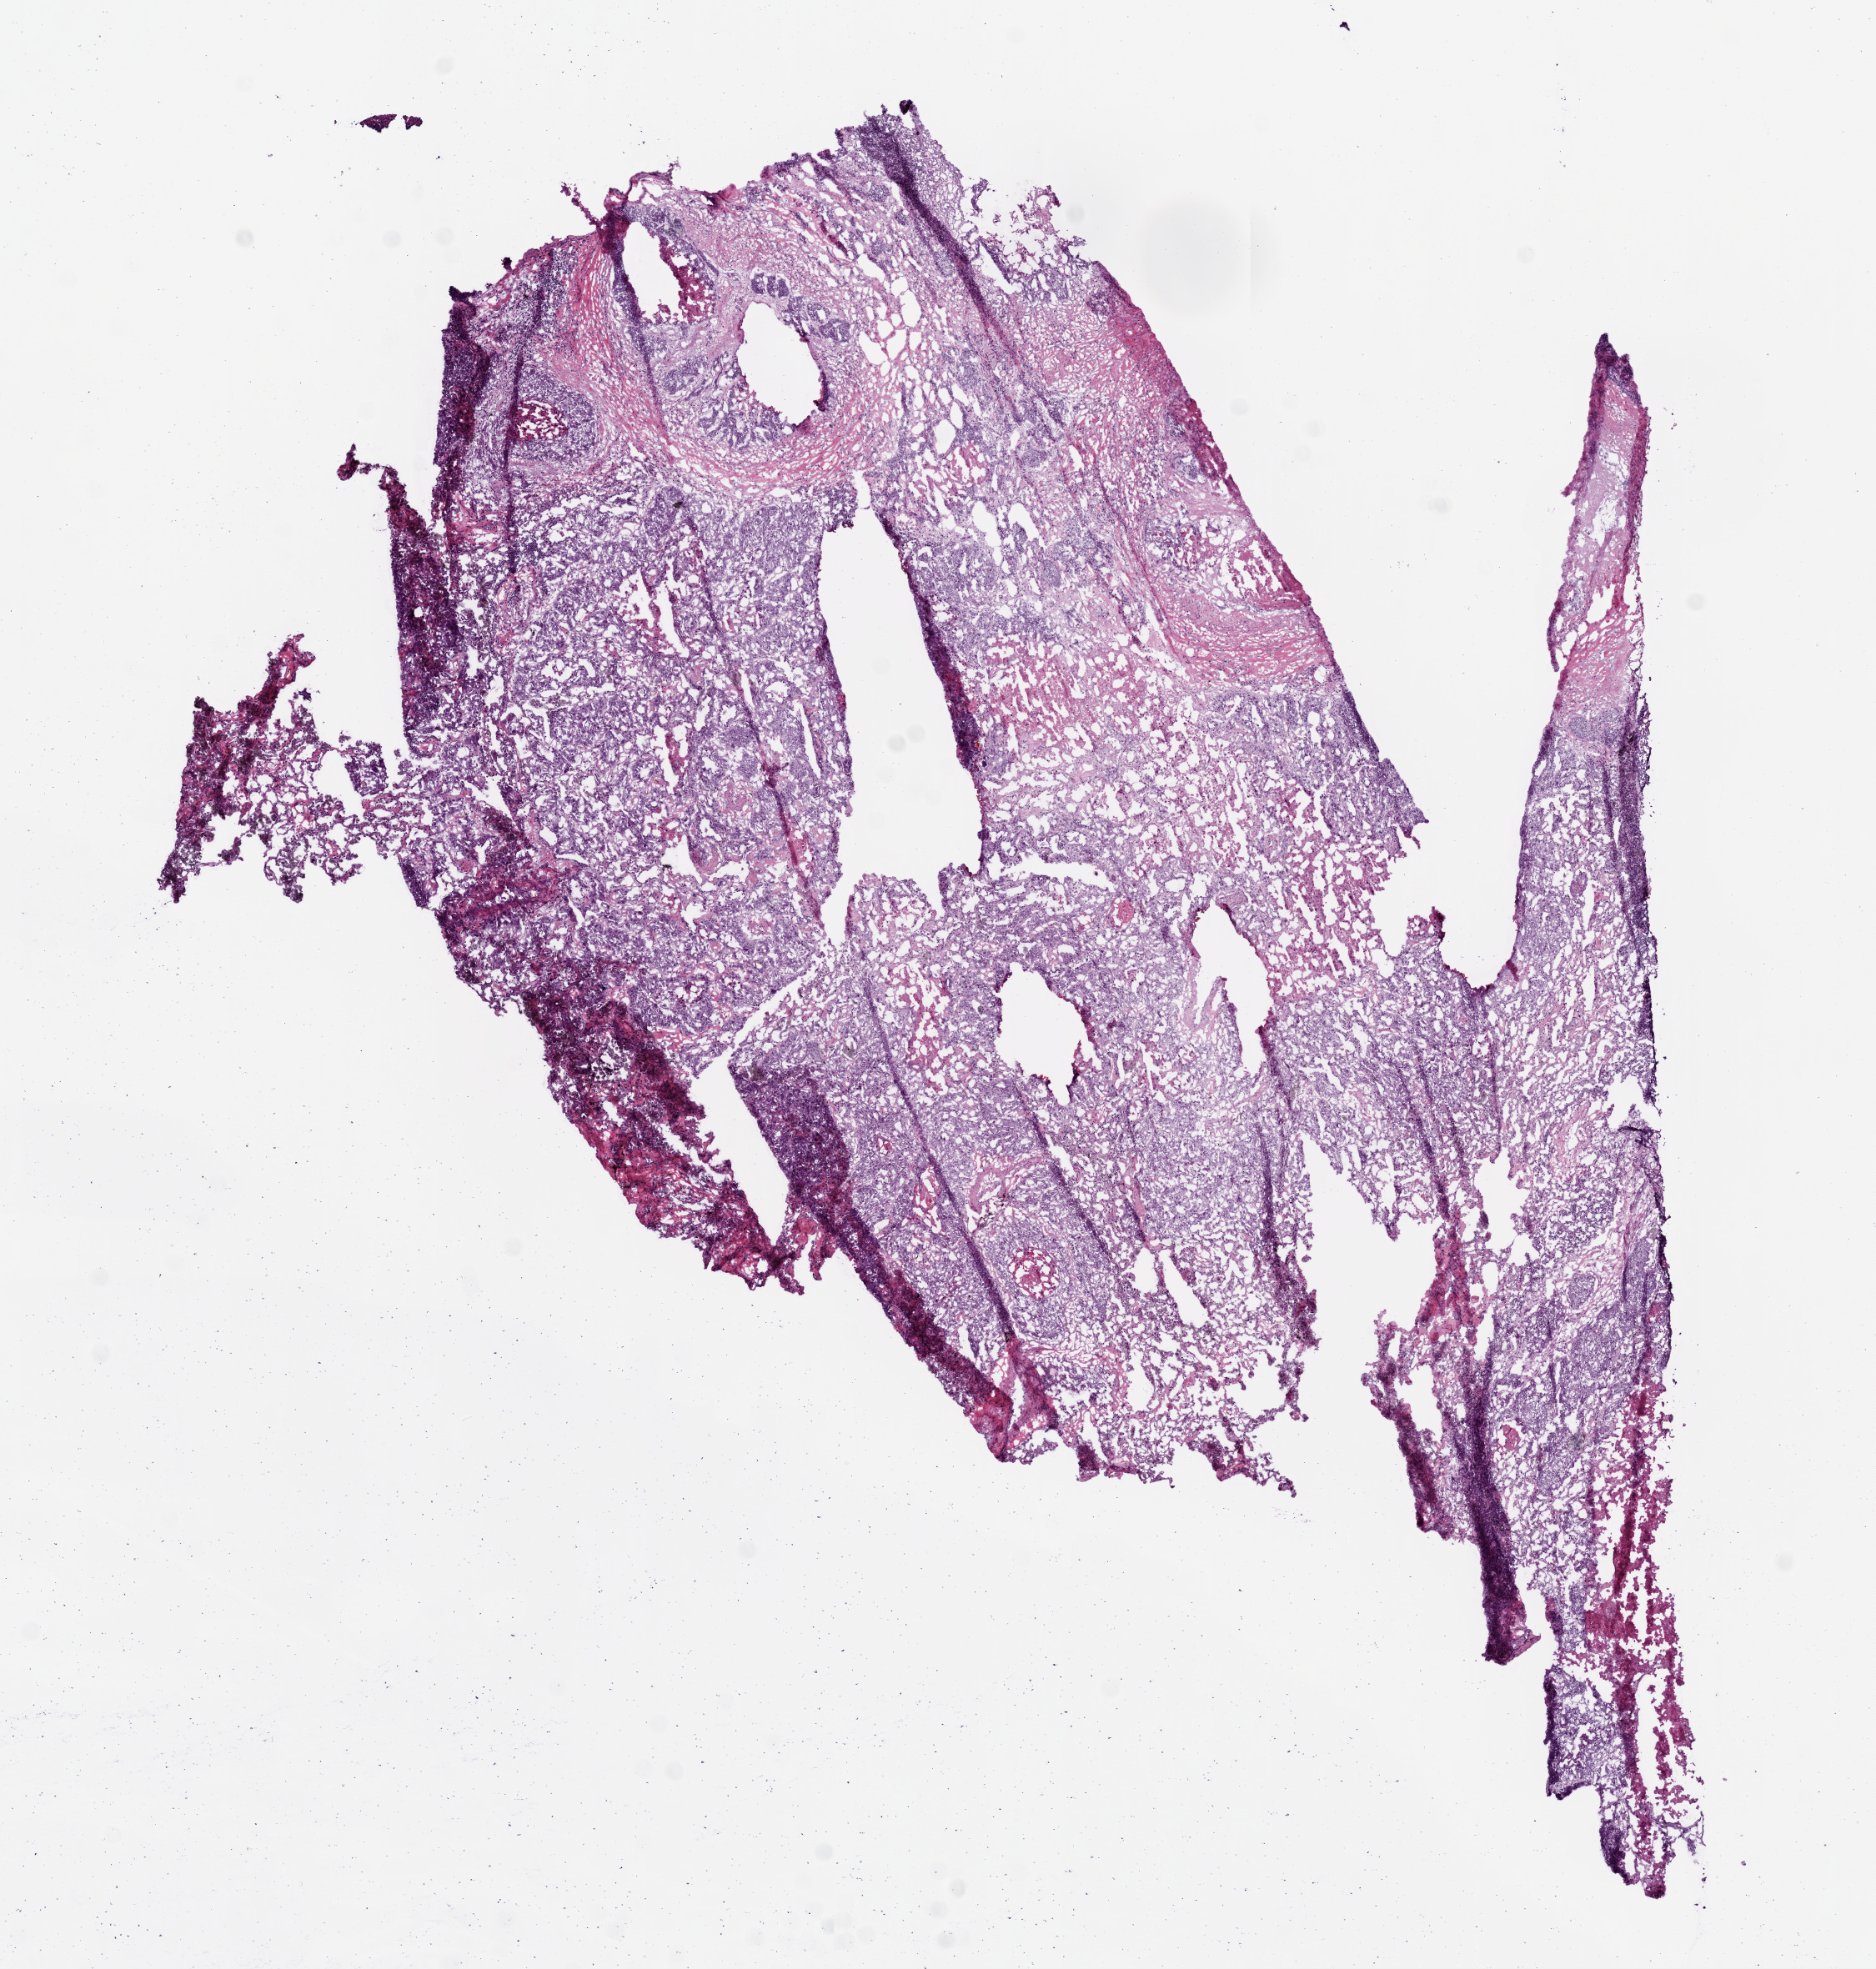
Whole-slide histology image, H&E — low-resolution overview of the scanned area, about 9.0 x 9.5 mm. Frozen section from the top of the tissue portion. Sample: primary tumour, lung. Male, age 53 years at initial diagnosis. Composition of this section per pathologist review: tumour cells 80%, tumour nuclei 70%, normal cells 10%, stromal cells 0%, necrosis 10%. Inflammatory infiltration, as recorded: lymphocyte infiltration 5%, monocyte infiltration 0%, neutrophil infiltration 0%.
Pathologic diagnosis: Squamous cell carcinoma, NOS (upper lobe, lung). AJCC pathologic stage: IIB.